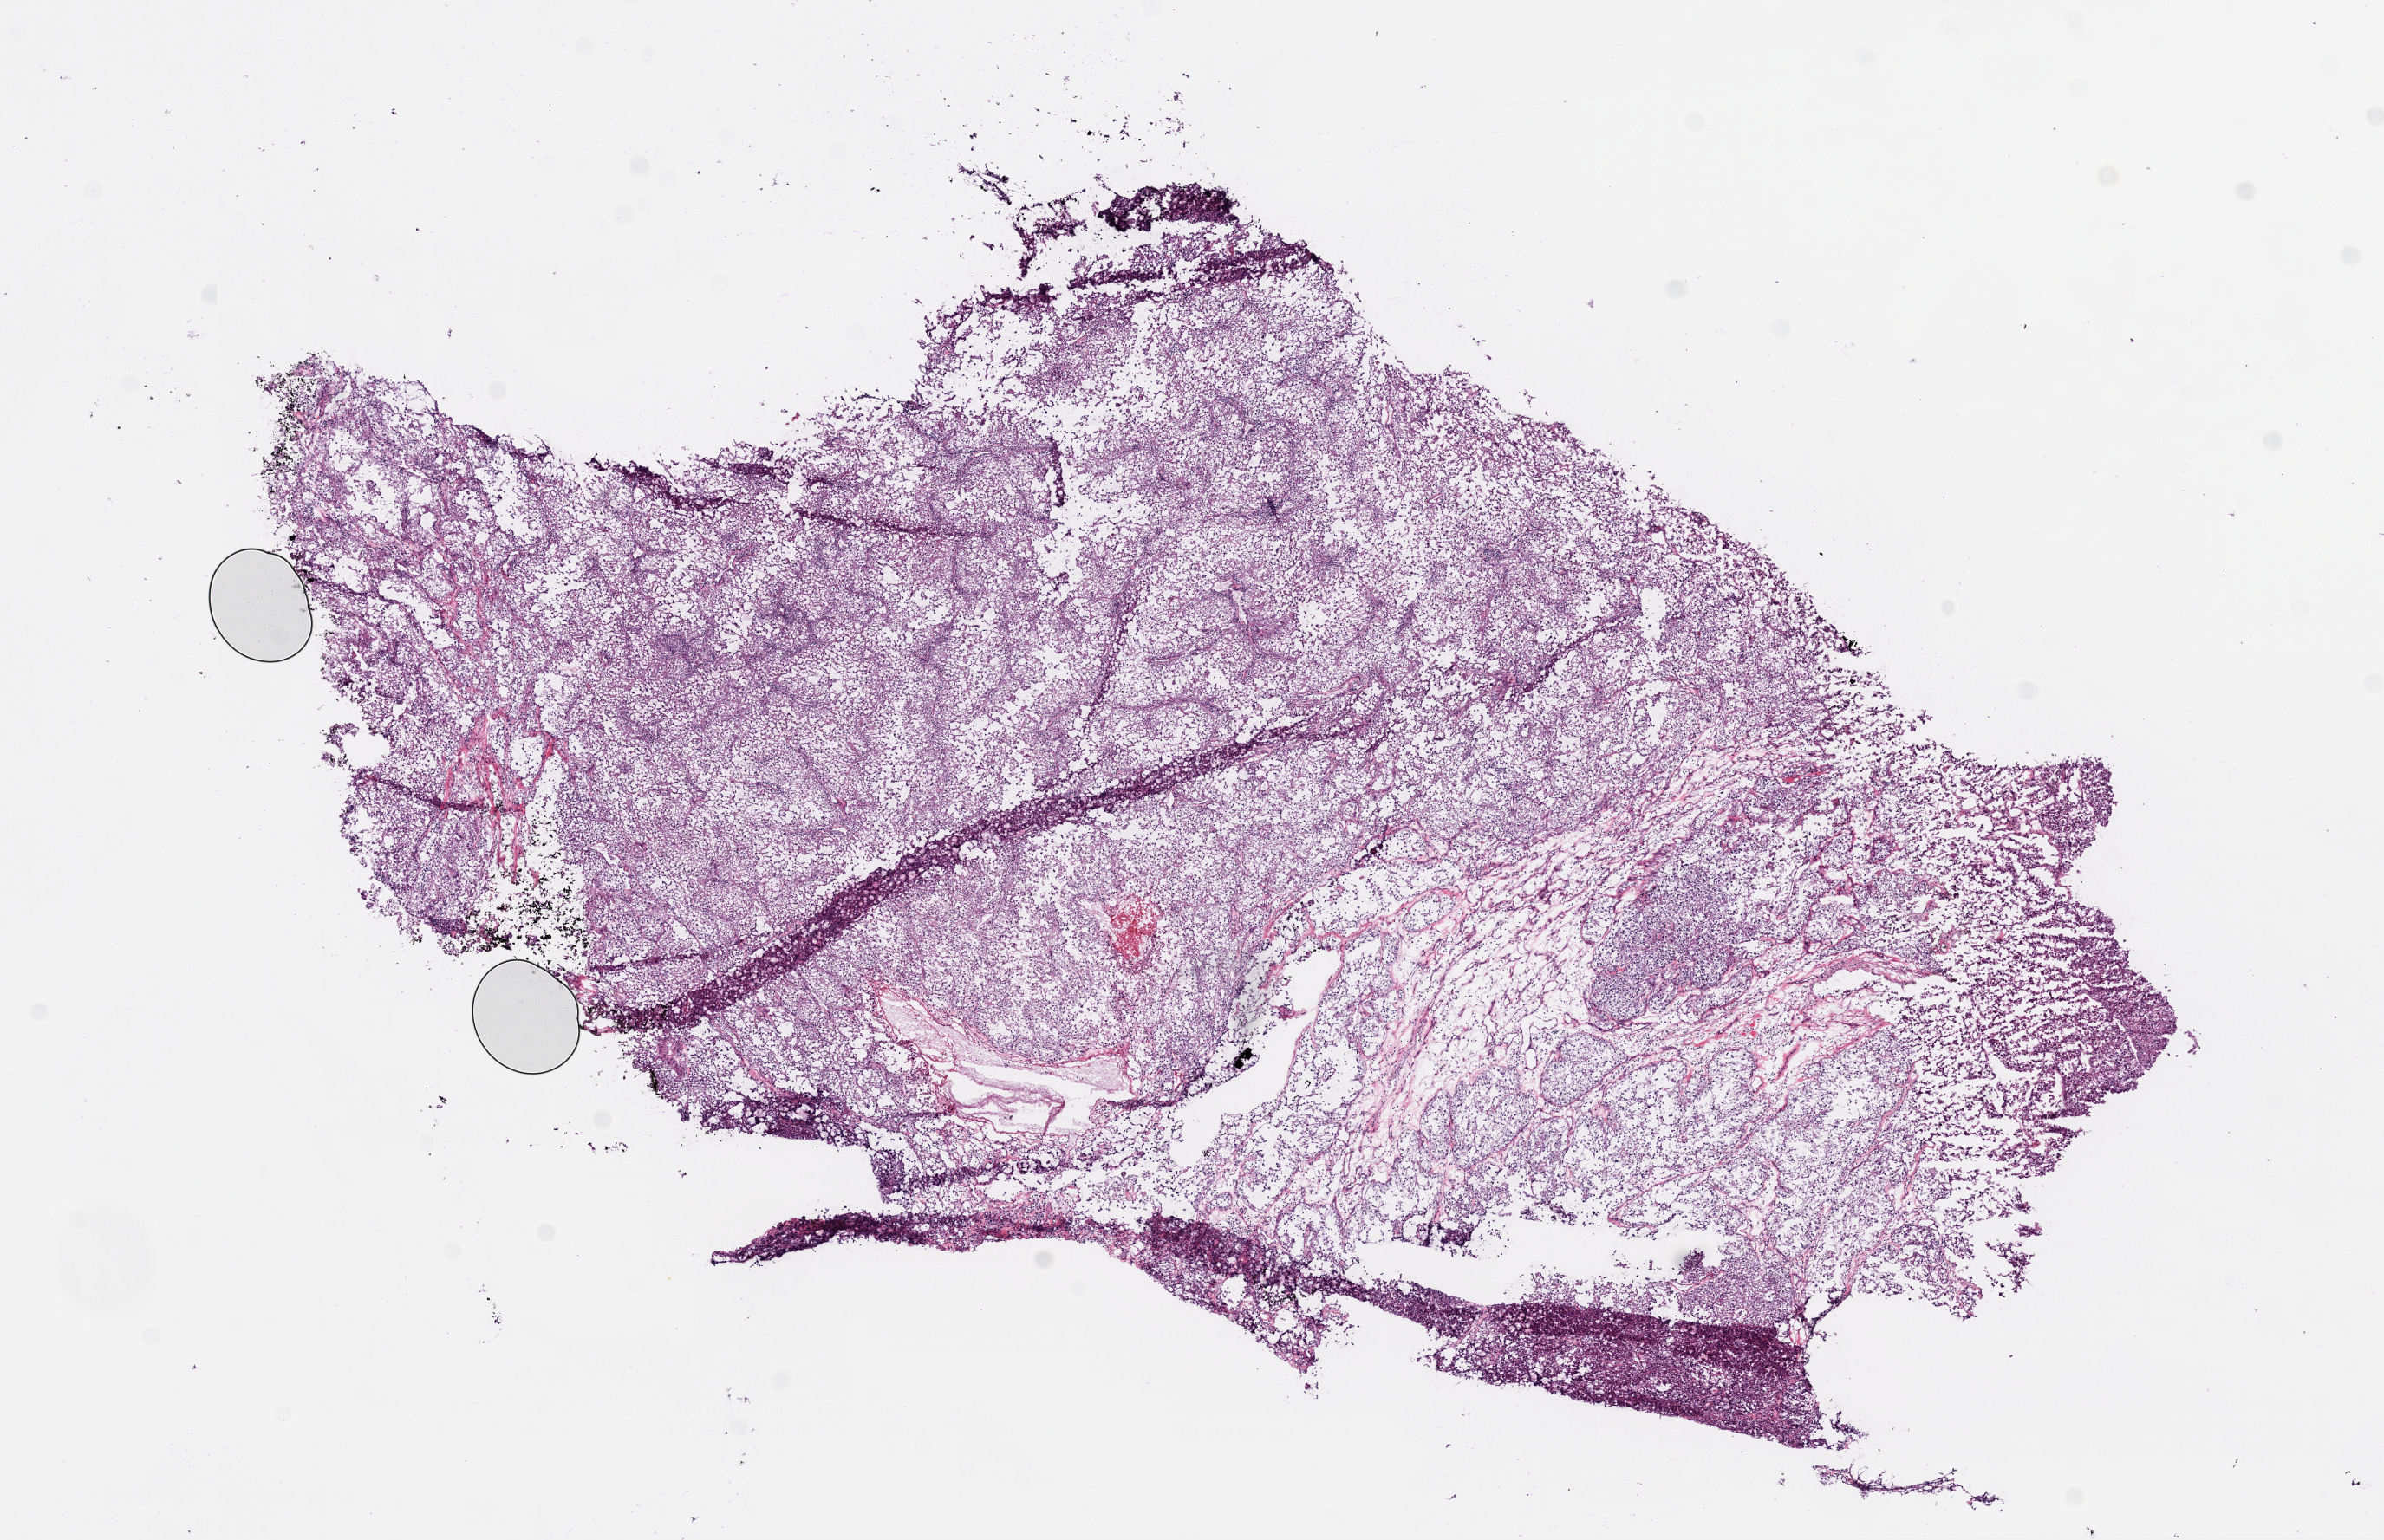
Whole-slide histology image, H&E-stained, shown as a low-resolution overview of the whole scanned area (about 11.0 x 7.1 mm, acquisition: 20x scan). Frozen section from the bottom of the tissue portion. Primary tumour sample from the kidney. Male, age 41 years at initial diagnosis. Histologic grade: G4 (undifferentiated). Pathologist review of this section (percent, as recorded): tumour cells 90%, tumour nuclei 80%, normal cells 0%, stromal cells 5%, necrosis 5%.
• histologic diagnosis: Clear cell adenocarcinoma, NOS
• laterality: right
• AJCC pathologic stage: II